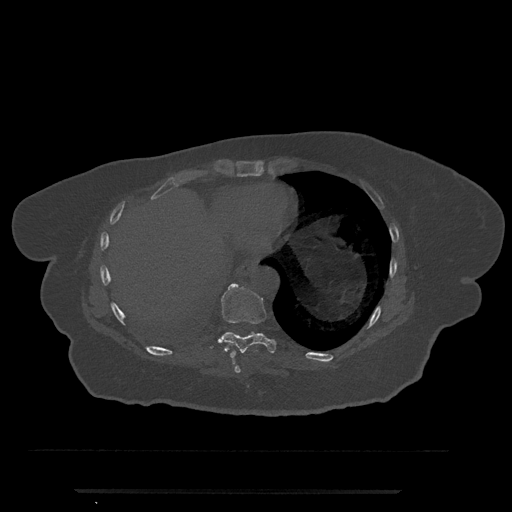
CT including the spine, one axial slice; position 334 of 797 along the scan axis; bone window (W 1800 / L 400 HU); 0.5 mm slice thickness; 512 × 512 image matrix, field of view 440 × 440 mm. Female patient, age 51 years. Case-level facts recorded for this patient, not image findings: primary cancer: neuro; vertebrae with lytic lesions (as recorded): T8.
Outlined on this slice (semi-automatic segmentation, software-assisted and operator-edited):
- T8 vertebra: bounding box (x1, y1, x2, y2) in pixels: (234, 365, 241, 373)
- T9 vertebra: (209, 283, 277, 358)